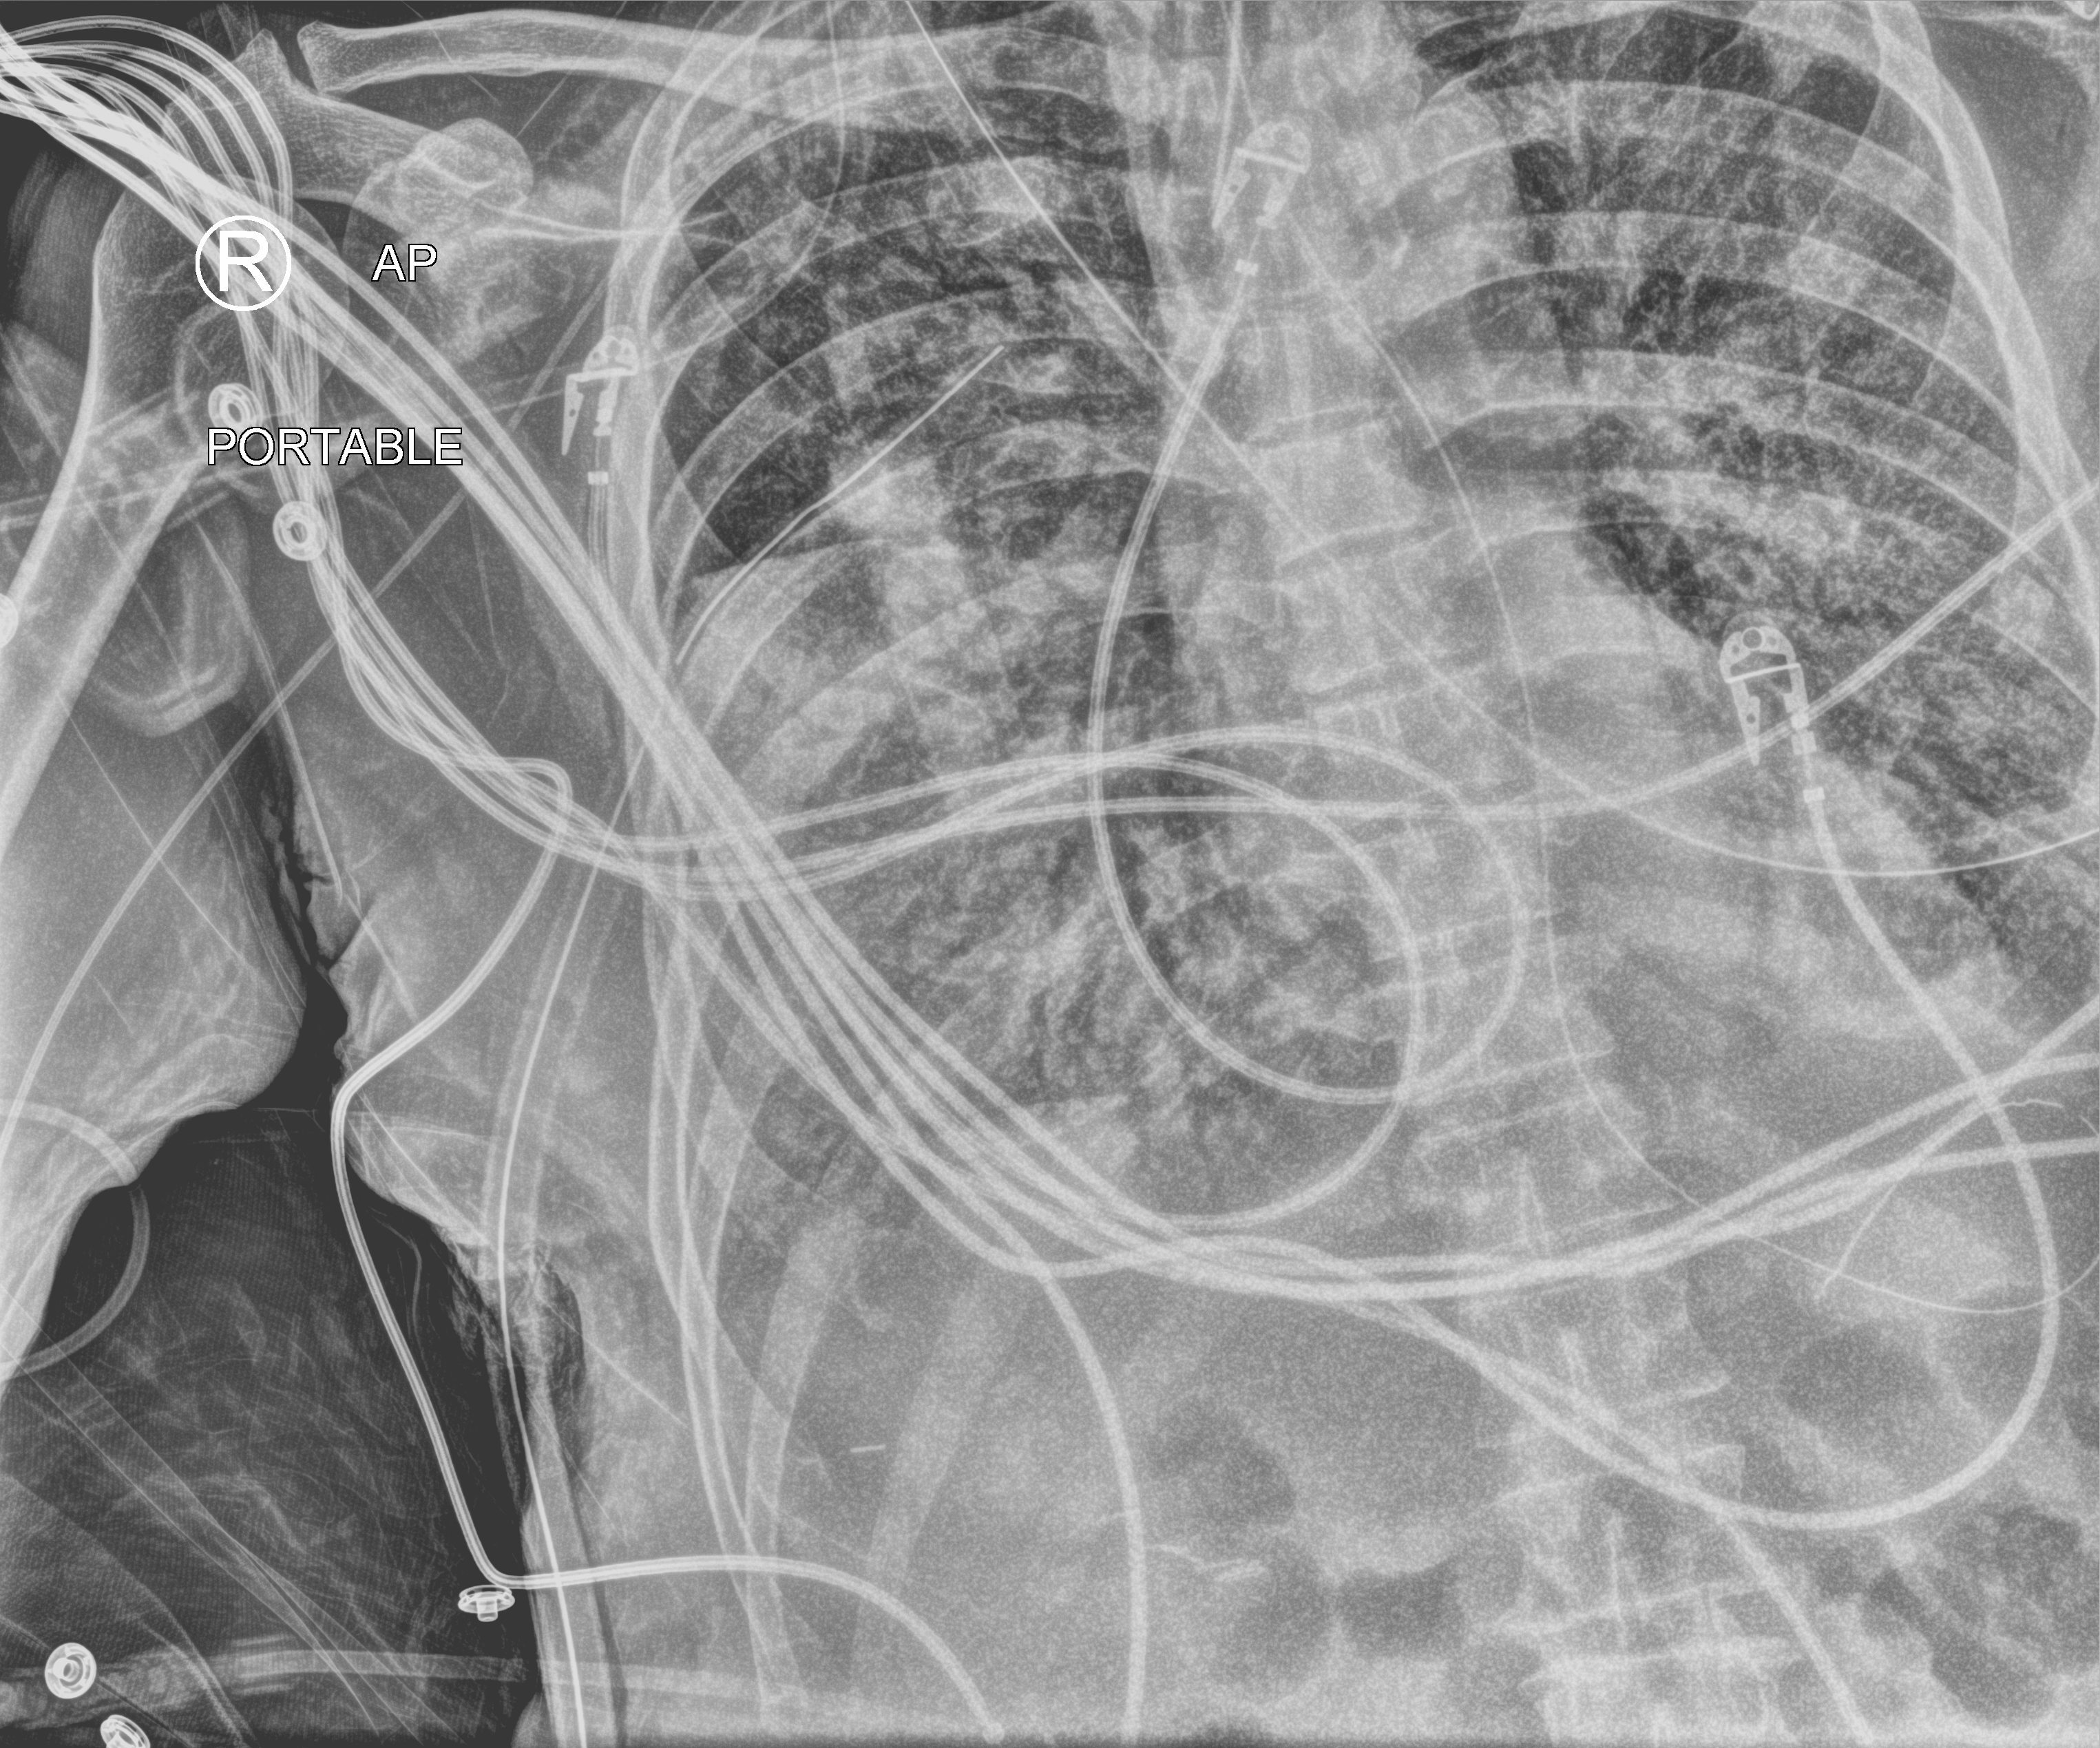
Chest X-ray (portable), anteroposterior (AP) projection. Male patient hospitalised with COVID-19, age 60–74 years.
Hospital-stay facts (about this admission, not read from this image; timing relative to this image not recorded):
- mechanically ventilated during this hospital stay: yes
- admitted to intensive care during this hospital stay: yes